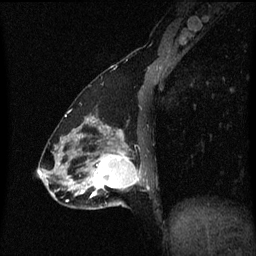
Breast MRI (dynamic contrast-enhanced), one sagittal slice. Position 22 of 60 along the scan axis. Dynamic contrast-enhanced series, image 2 of 3 at this slice position (ordered by acquisition). 1.5 T. TE 4.2 ms, TR 8.4 ms. 2 mm slice thickness. 256 × 256 image matrix. Female patient, age 47 years.
Annotated regions visible in this slice (semi-automatically segmented with operator editing):
- analysis volume of interest (the breast-tissue region the enhancement analysis was run in; not a lesion): bounding box (x1, y1, x2, y2) in pixels: (81, 138, 146, 209)
- tumour enhancement mask (voxels above the 70 % enhancement threshold inside the analysis volume of interest): (86, 138, 141, 199)